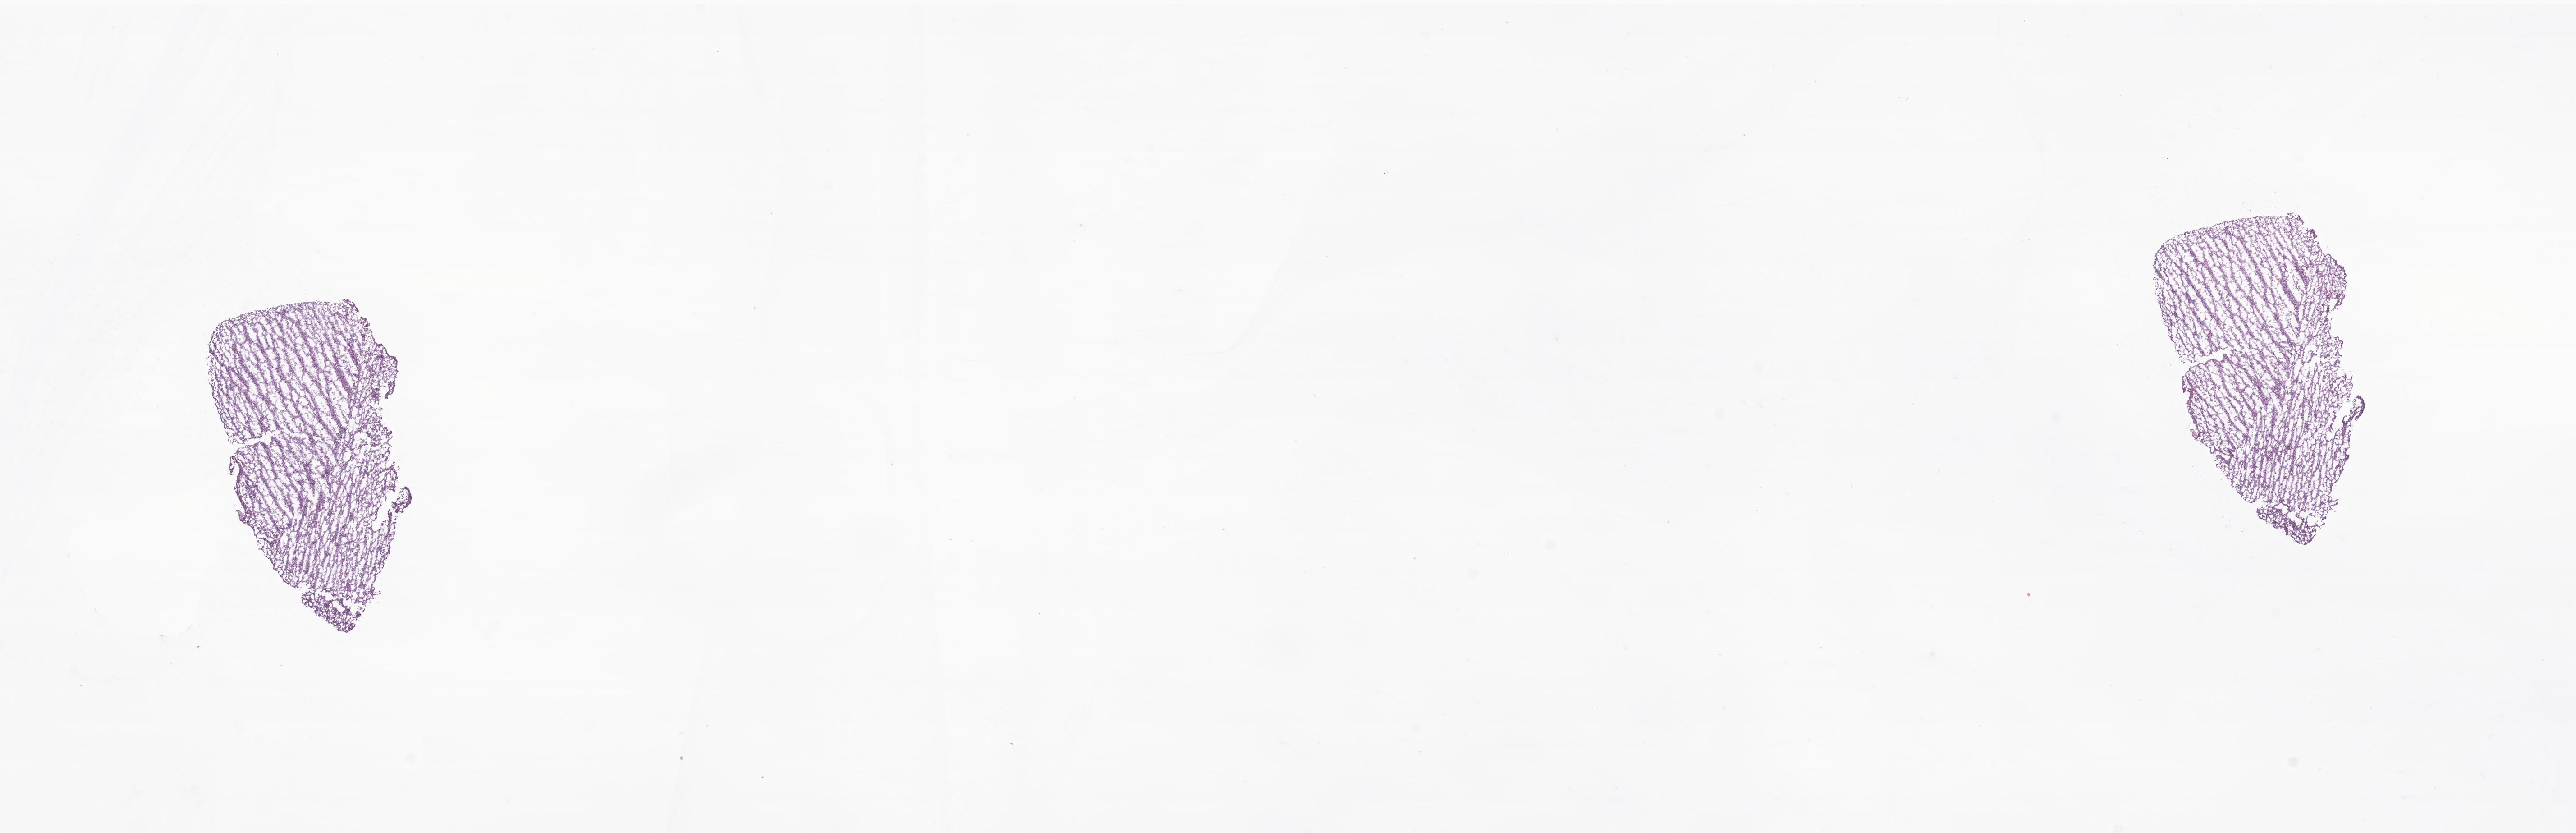
Whole-slide image, hematoxylin and eosin (H&E) stain of tumor tissue from the frontal lobe, a low-resolution overview of the entire scanned area, about 24.1 x 7.8 mm. Cryosection (OCT / tissue freezing medium). Patient: female, age 13 days.
- diagnosis: Neoplasm, uncertain whether benign or malignant